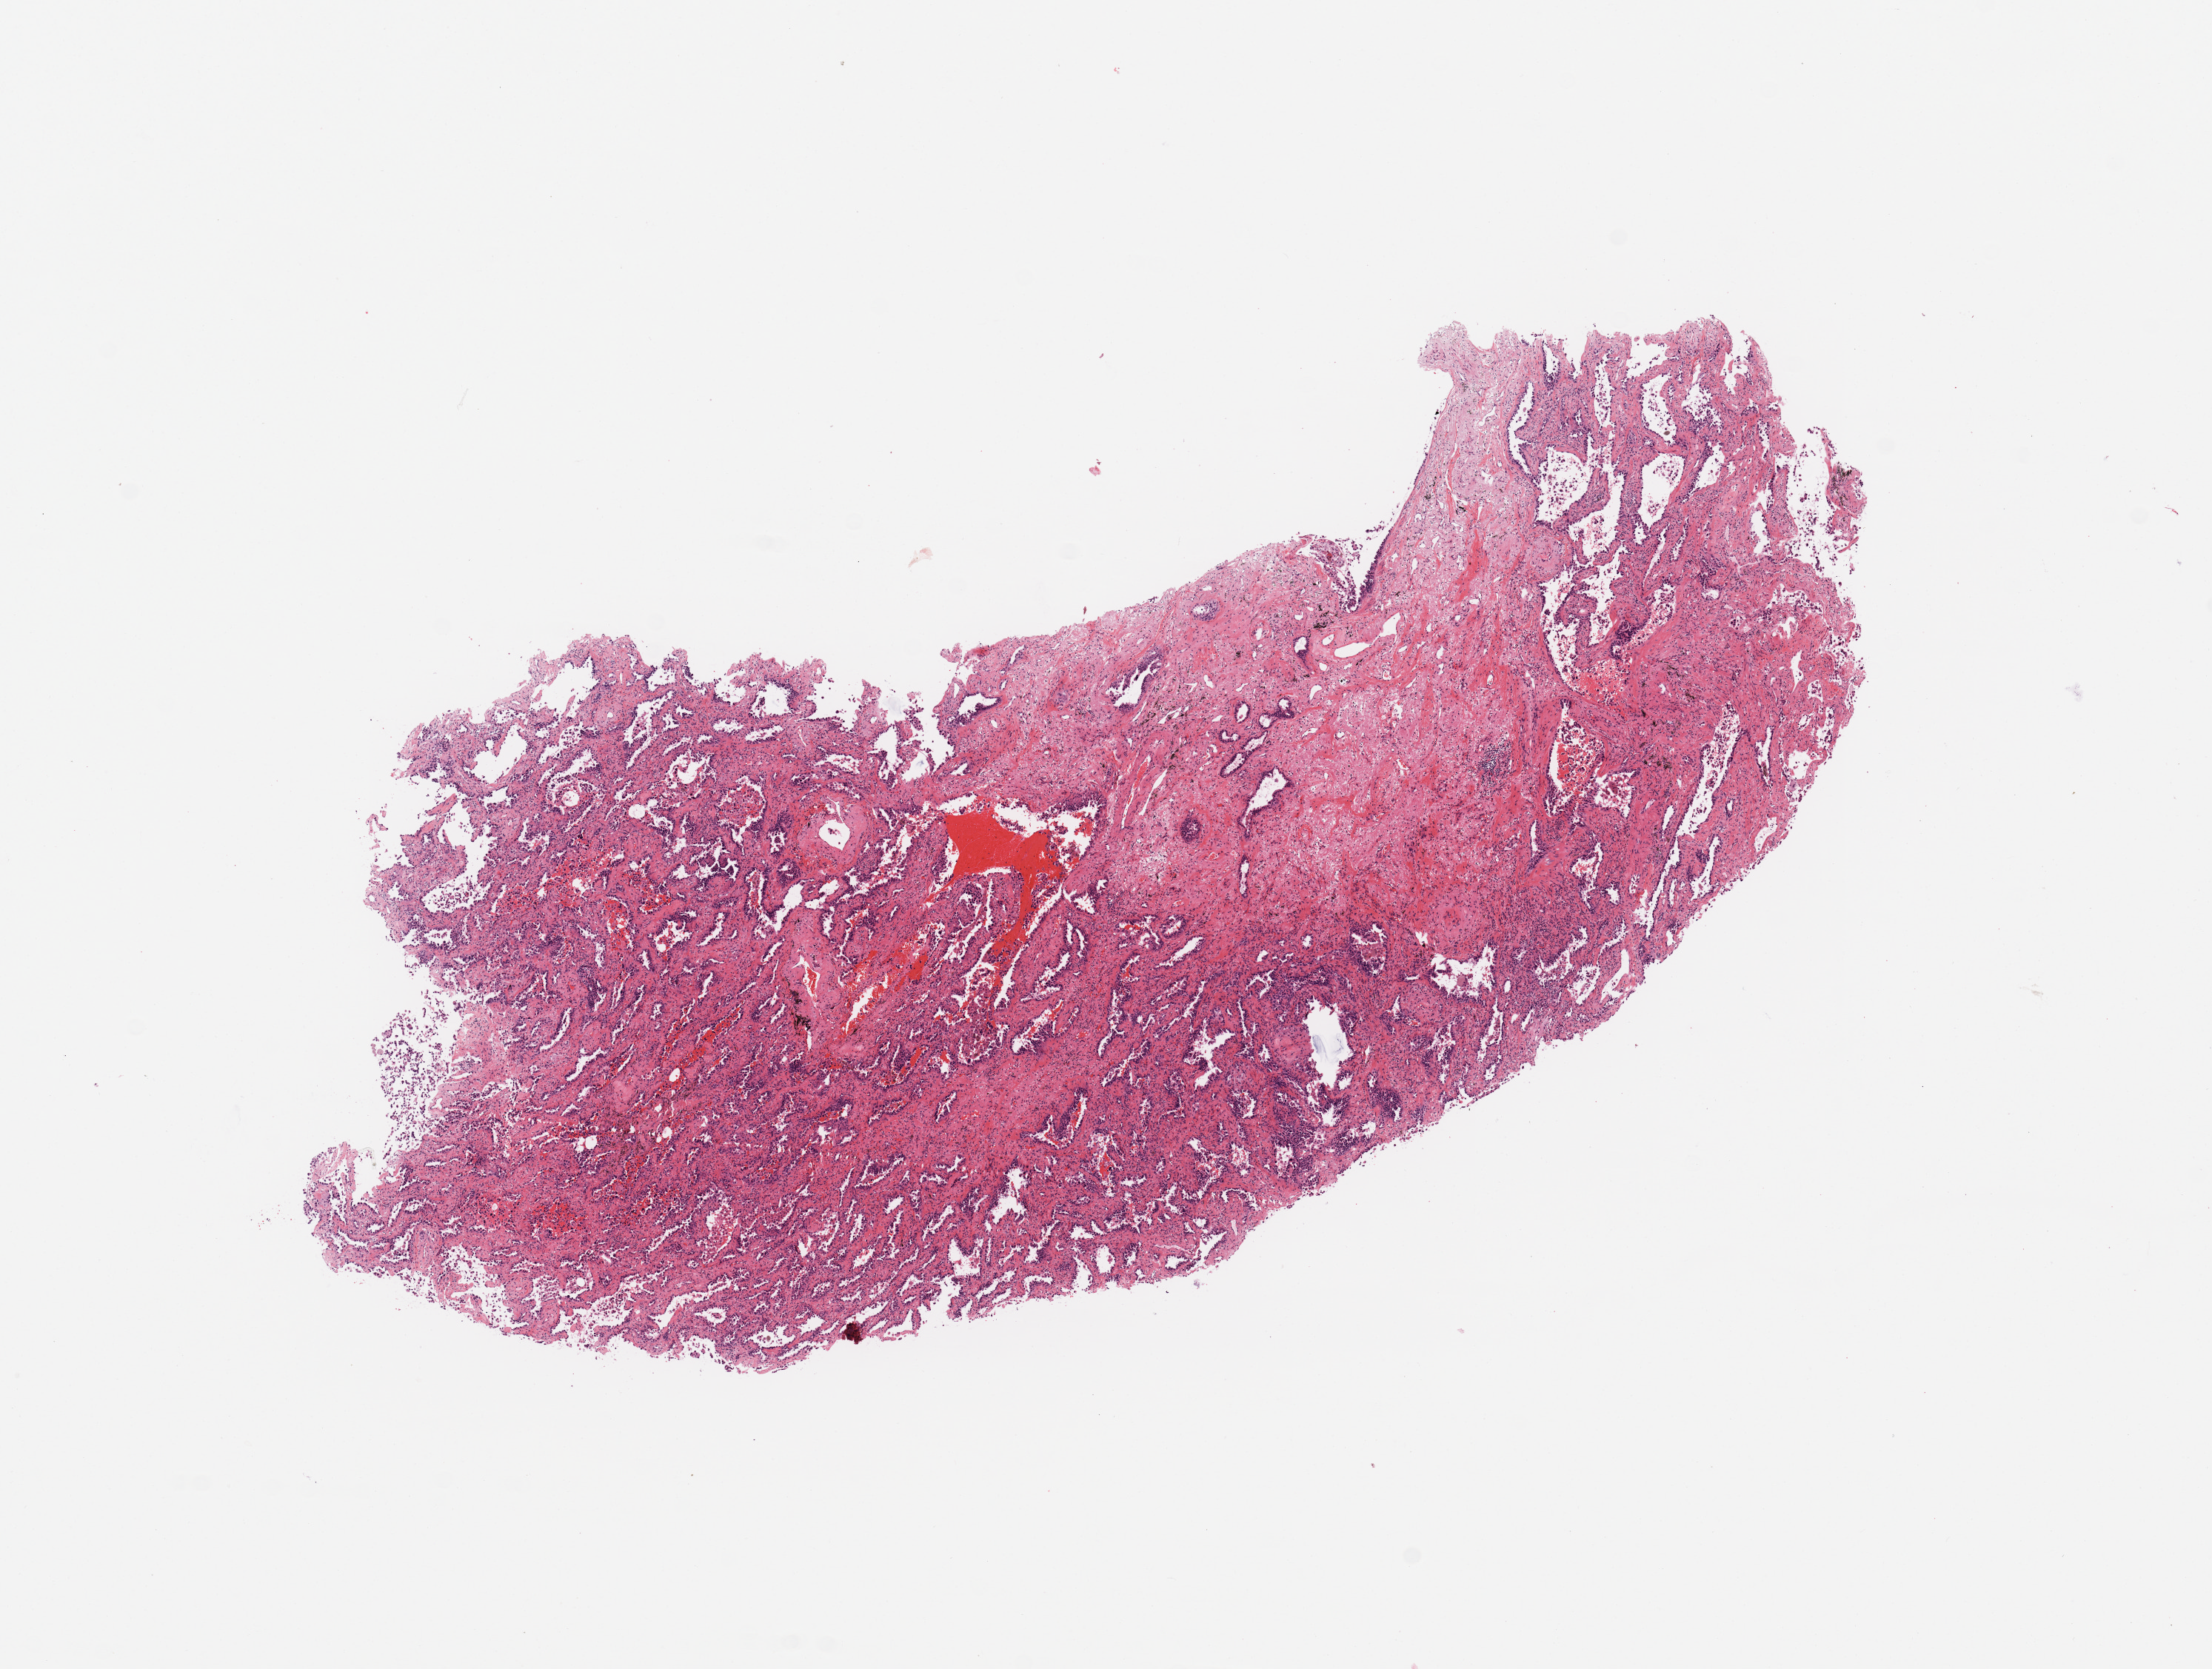
Whole-slide histology image, H&E — whole scanned area (about 11.8 x 8.9 mm) shown as a low-resolution overview; tumour tissue sample, sampled site: lung. Patient: male, age 76 years. Histologic grade: G2 (moderately differentiated). Slide review estimates, as recorded: tumour nuclei 70%, necrosis 8%.
AJCC pathologic stage: IA. Histologic diagnosis: Adenocarcinoma, NOS. Primary tumour site (as recorded): right upper lobe.